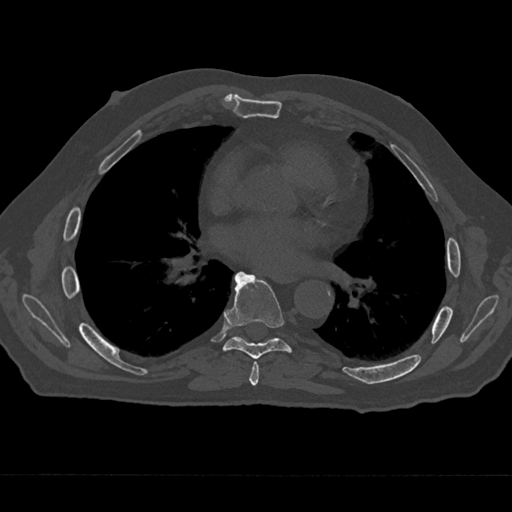
CT including the spine, one axial slice. Slice 368 of 797 in the series (ordered by position). 120 kVp. Bone window (W 1800 / L 400 HU). 0.5 mm slice thickness. 512 × 512 image matrix, field of view 377 × 377 mm. Male patient, age 75 years. Case-level facts recorded for this patient, not image findings: primary cancer: renal; vertebrae with lytic lesions (as recorded): T4.
Structures marked on this image (semi-automatically segmented with operator editing):
- T6 vertebra: bounding box (x1, y1, x2, y2) in pixels: (249, 361, 259, 386)
- T7 vertebra: (215, 272, 291, 359)